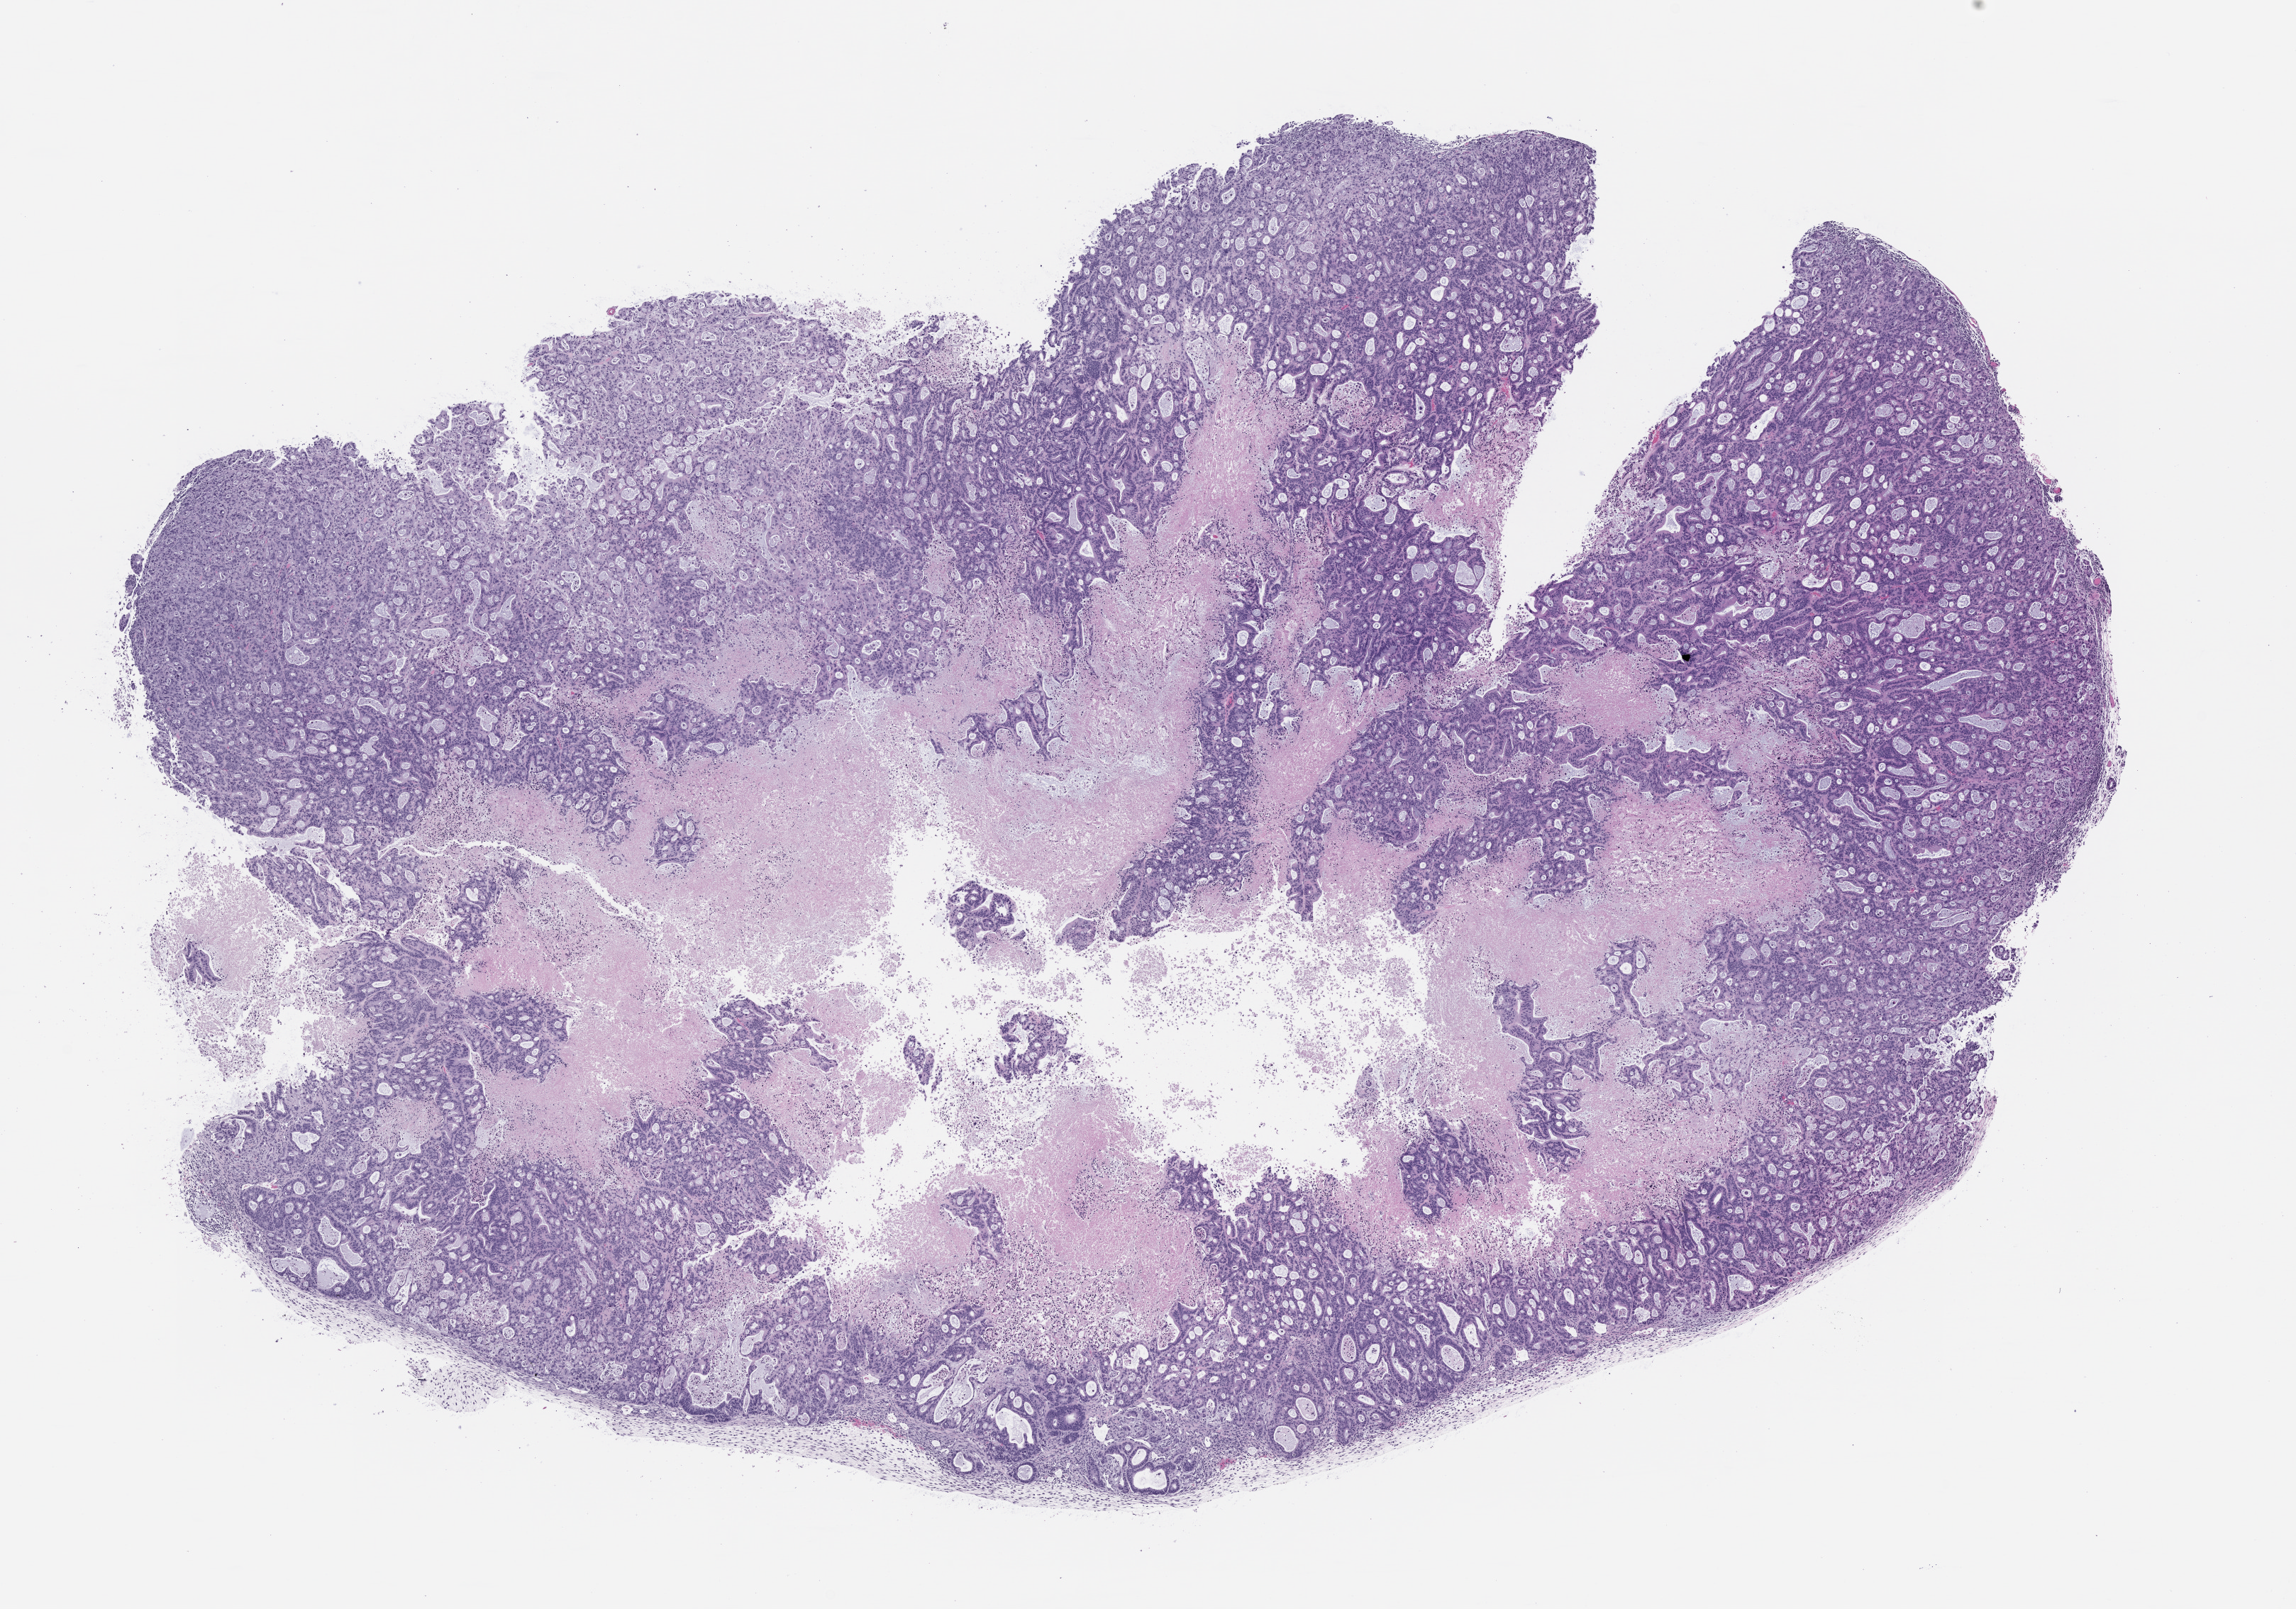
Whole-slide image, hematoxylin and eosin (H&E): patient-derived xenograft (human tumor grown in a mouse) — whole scanned area (about 13.0 x 9.1 mm) shown as a low-resolution overview; formalin-fixed, paraffin-embedded (FFPE) tissue; originating tumor site category: pancreas.
Originating patient diagnosis: Pancreatic Adenocarcinoma.